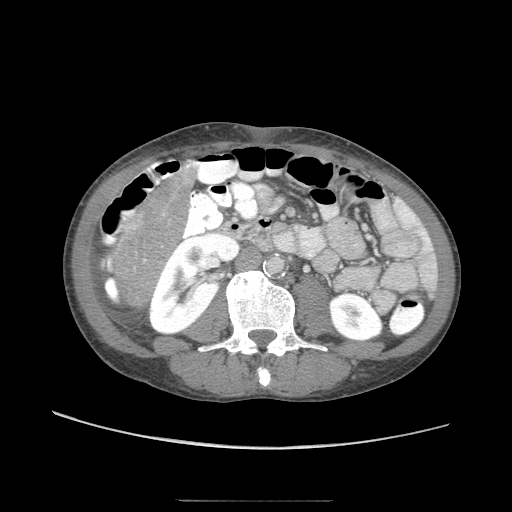
Contrast-enhanced abdominal CT (liver protocol), one axial slice. Position 11 of 103 along the scan axis. 120 kVp. Soft-tissue window (W 400 / L 40 HU). 512 × 512 image matrix, field of view 380 × 380 mm. From the clinical record (not read from this slice): diagnosis: hepatocellular carcinoma (patient treated with transarterial chemoembolisation; whether this scan precedes or follows treatment is not stated here); TNM stage (as recorded): Stage-IIIA; Child-Pugh class: A; tumour differentiation: moderately differentiated; tumour nodularity: multinodular.
Structures marked on this image (semi-automatic segmentation, software-assisted and operator-edited):
- liver parenchyma outside the tumour (the mass and vessels are separate outlines, so this box may not span the whole liver): bounding box <101,203,158,308> (left, top, right, bottom; pixels)
- mass: <104,204,145,262>